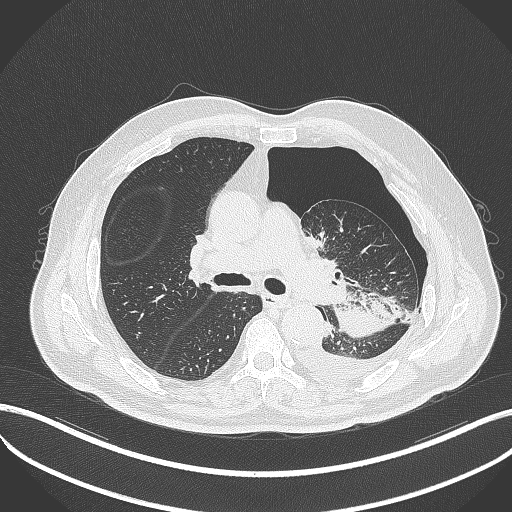
Chest CT, one axial slice. Position 317 of 464 along the scan axis. 120 kVp. Lung window (W 1500 / L -600 HU). 1 mm slice thickness. 512 × 512 image matrix. Patient: male, 76 years. From the clinical record (not read from this slice): clinical TNM (as recorded): T3 N0 M1b.
Structures marked on this image (bounding box drawn by a radiologist):
- lung tumour (recorded histology: adenocarcinoma): bounding box [x1, y1, x2, y2] px = [334, 299, 399, 337]